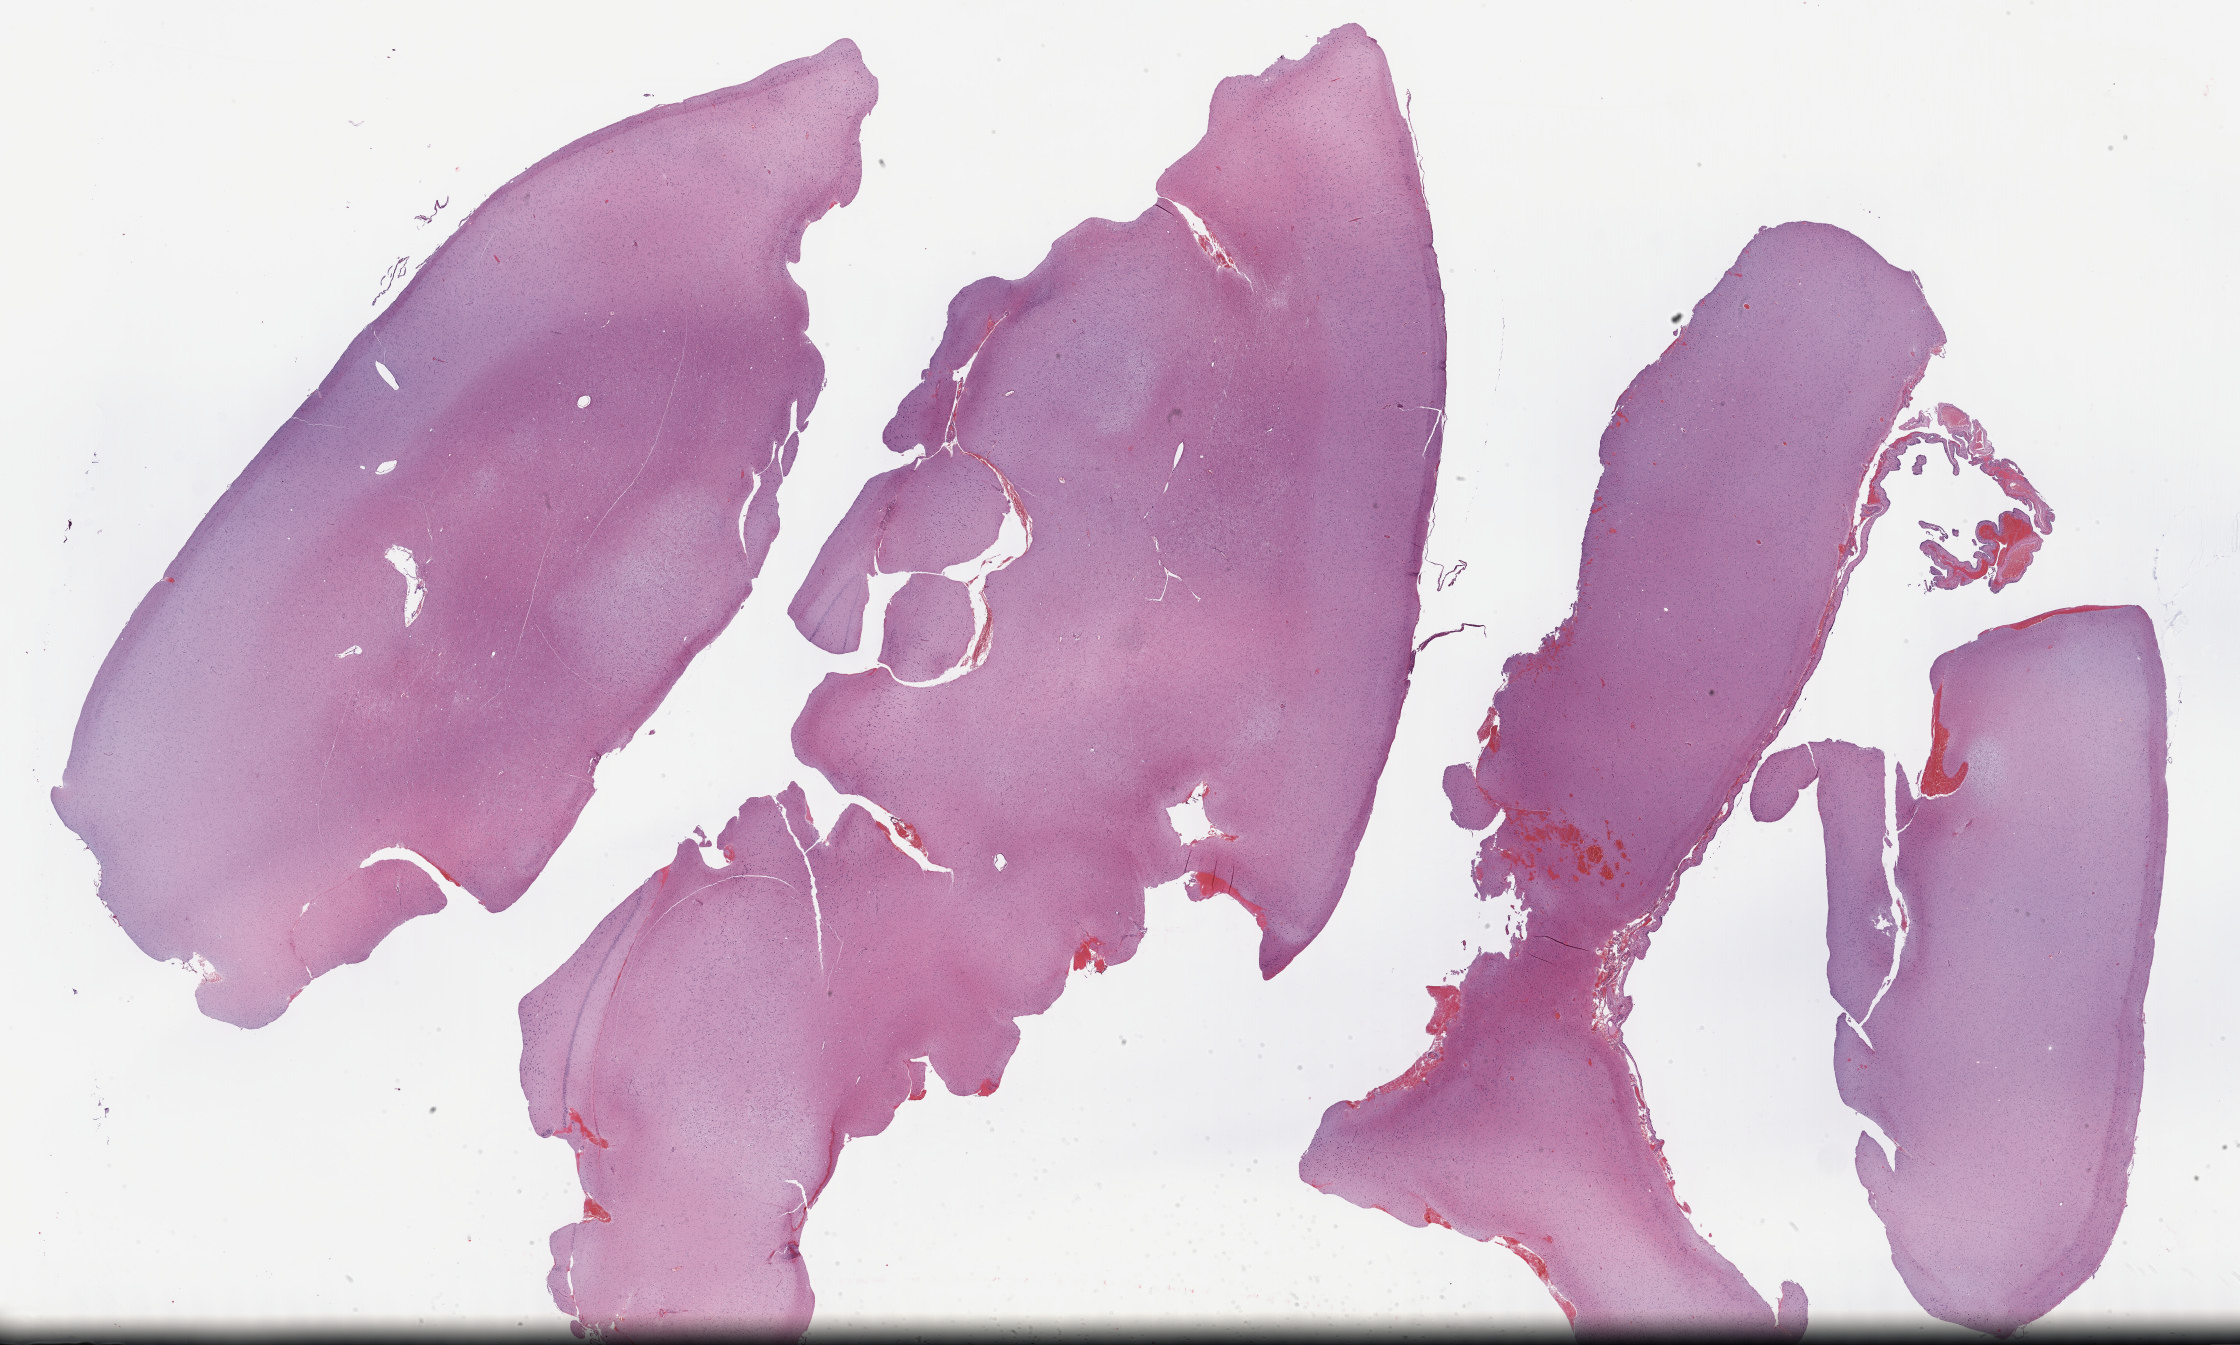
Whole-slide histology image, H&E — low-resolution overview of the scanned area, about 36.2 x 21.8 mm (slide scanned at 40x). Formalin-fixed paraffin-embedded (FFPE) diagnostic section. Sample: primary tumour, brain. Female, age 37 years at initial diagnosis. Histologic grade: G2 (moderately differentiated).
Laterality: left. Diagnosis: Astrocytoma, NOS (cerebrum).